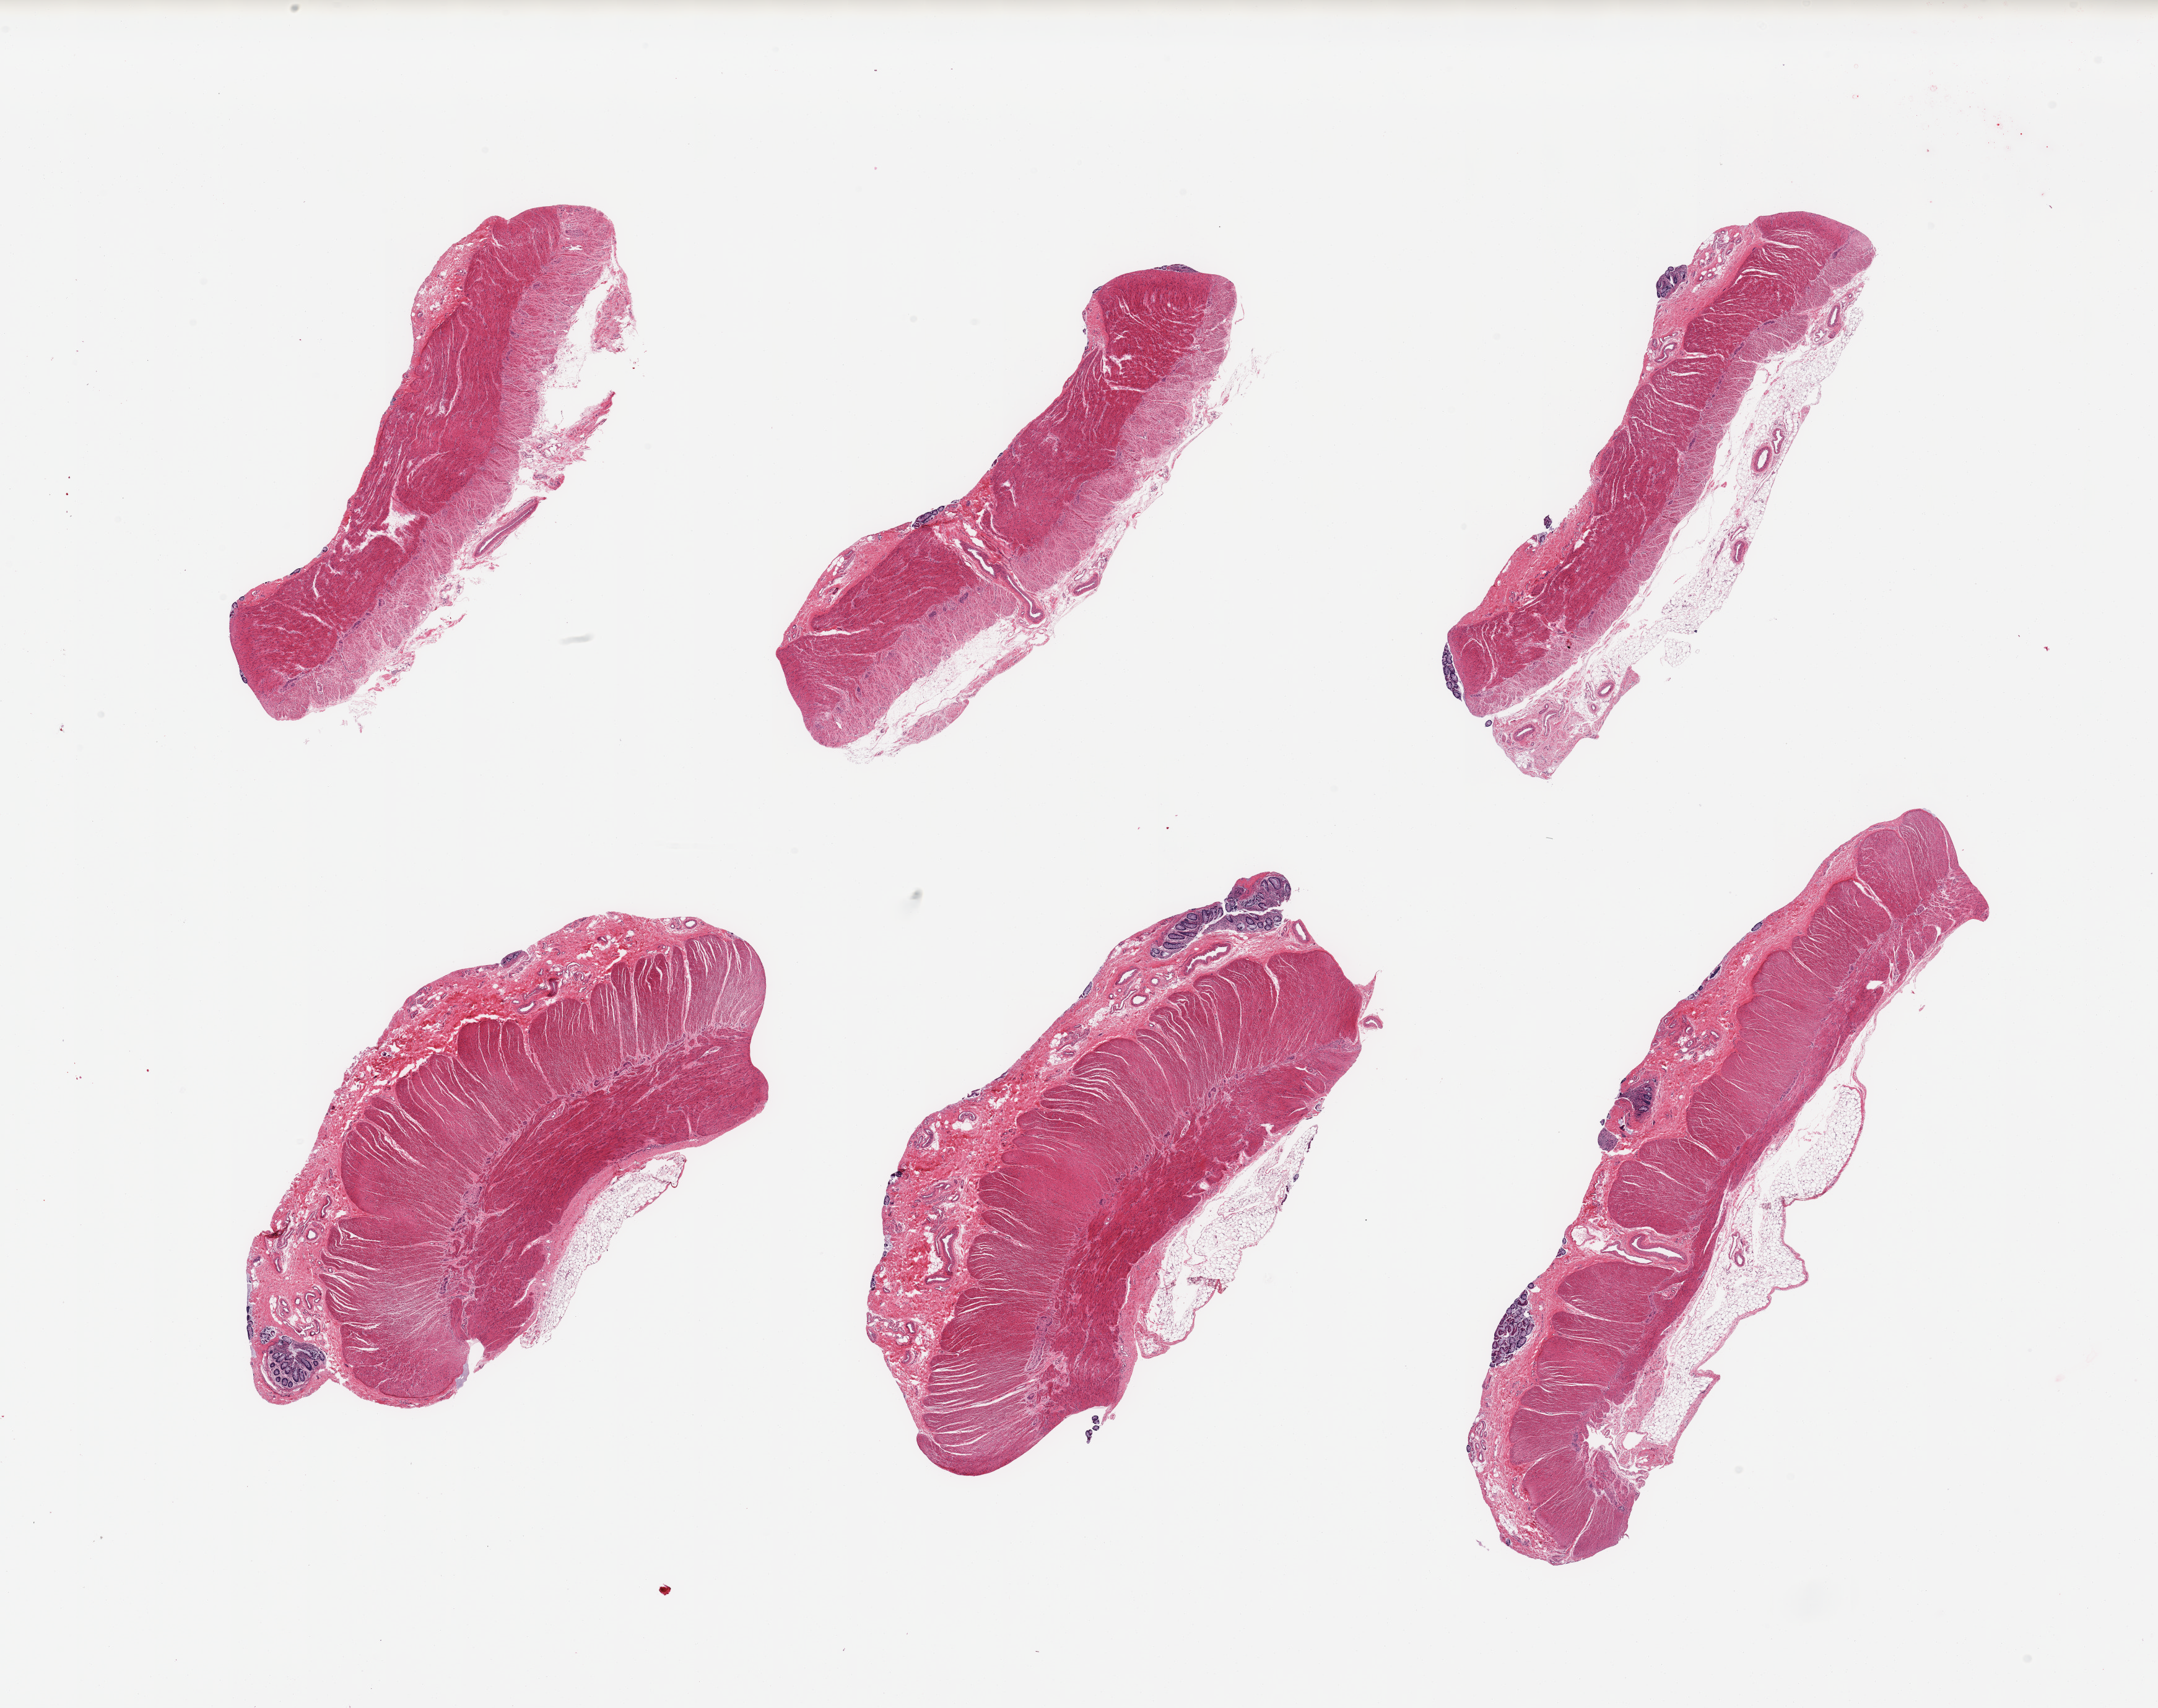
Whole-slide image, hematoxylin and eosin (H&E) stain — low-resolution overview of the scanned area, about 27.6 x 21.8 mm. PAXgene-fixed paraffin-embedded (PFPE) section. Sampled site (target tissue): sigmoid colon. Tissue donor sample. Donor sex: male.
Pathologist's review note for this sample: 6 pieces, confirmed target muscularis.